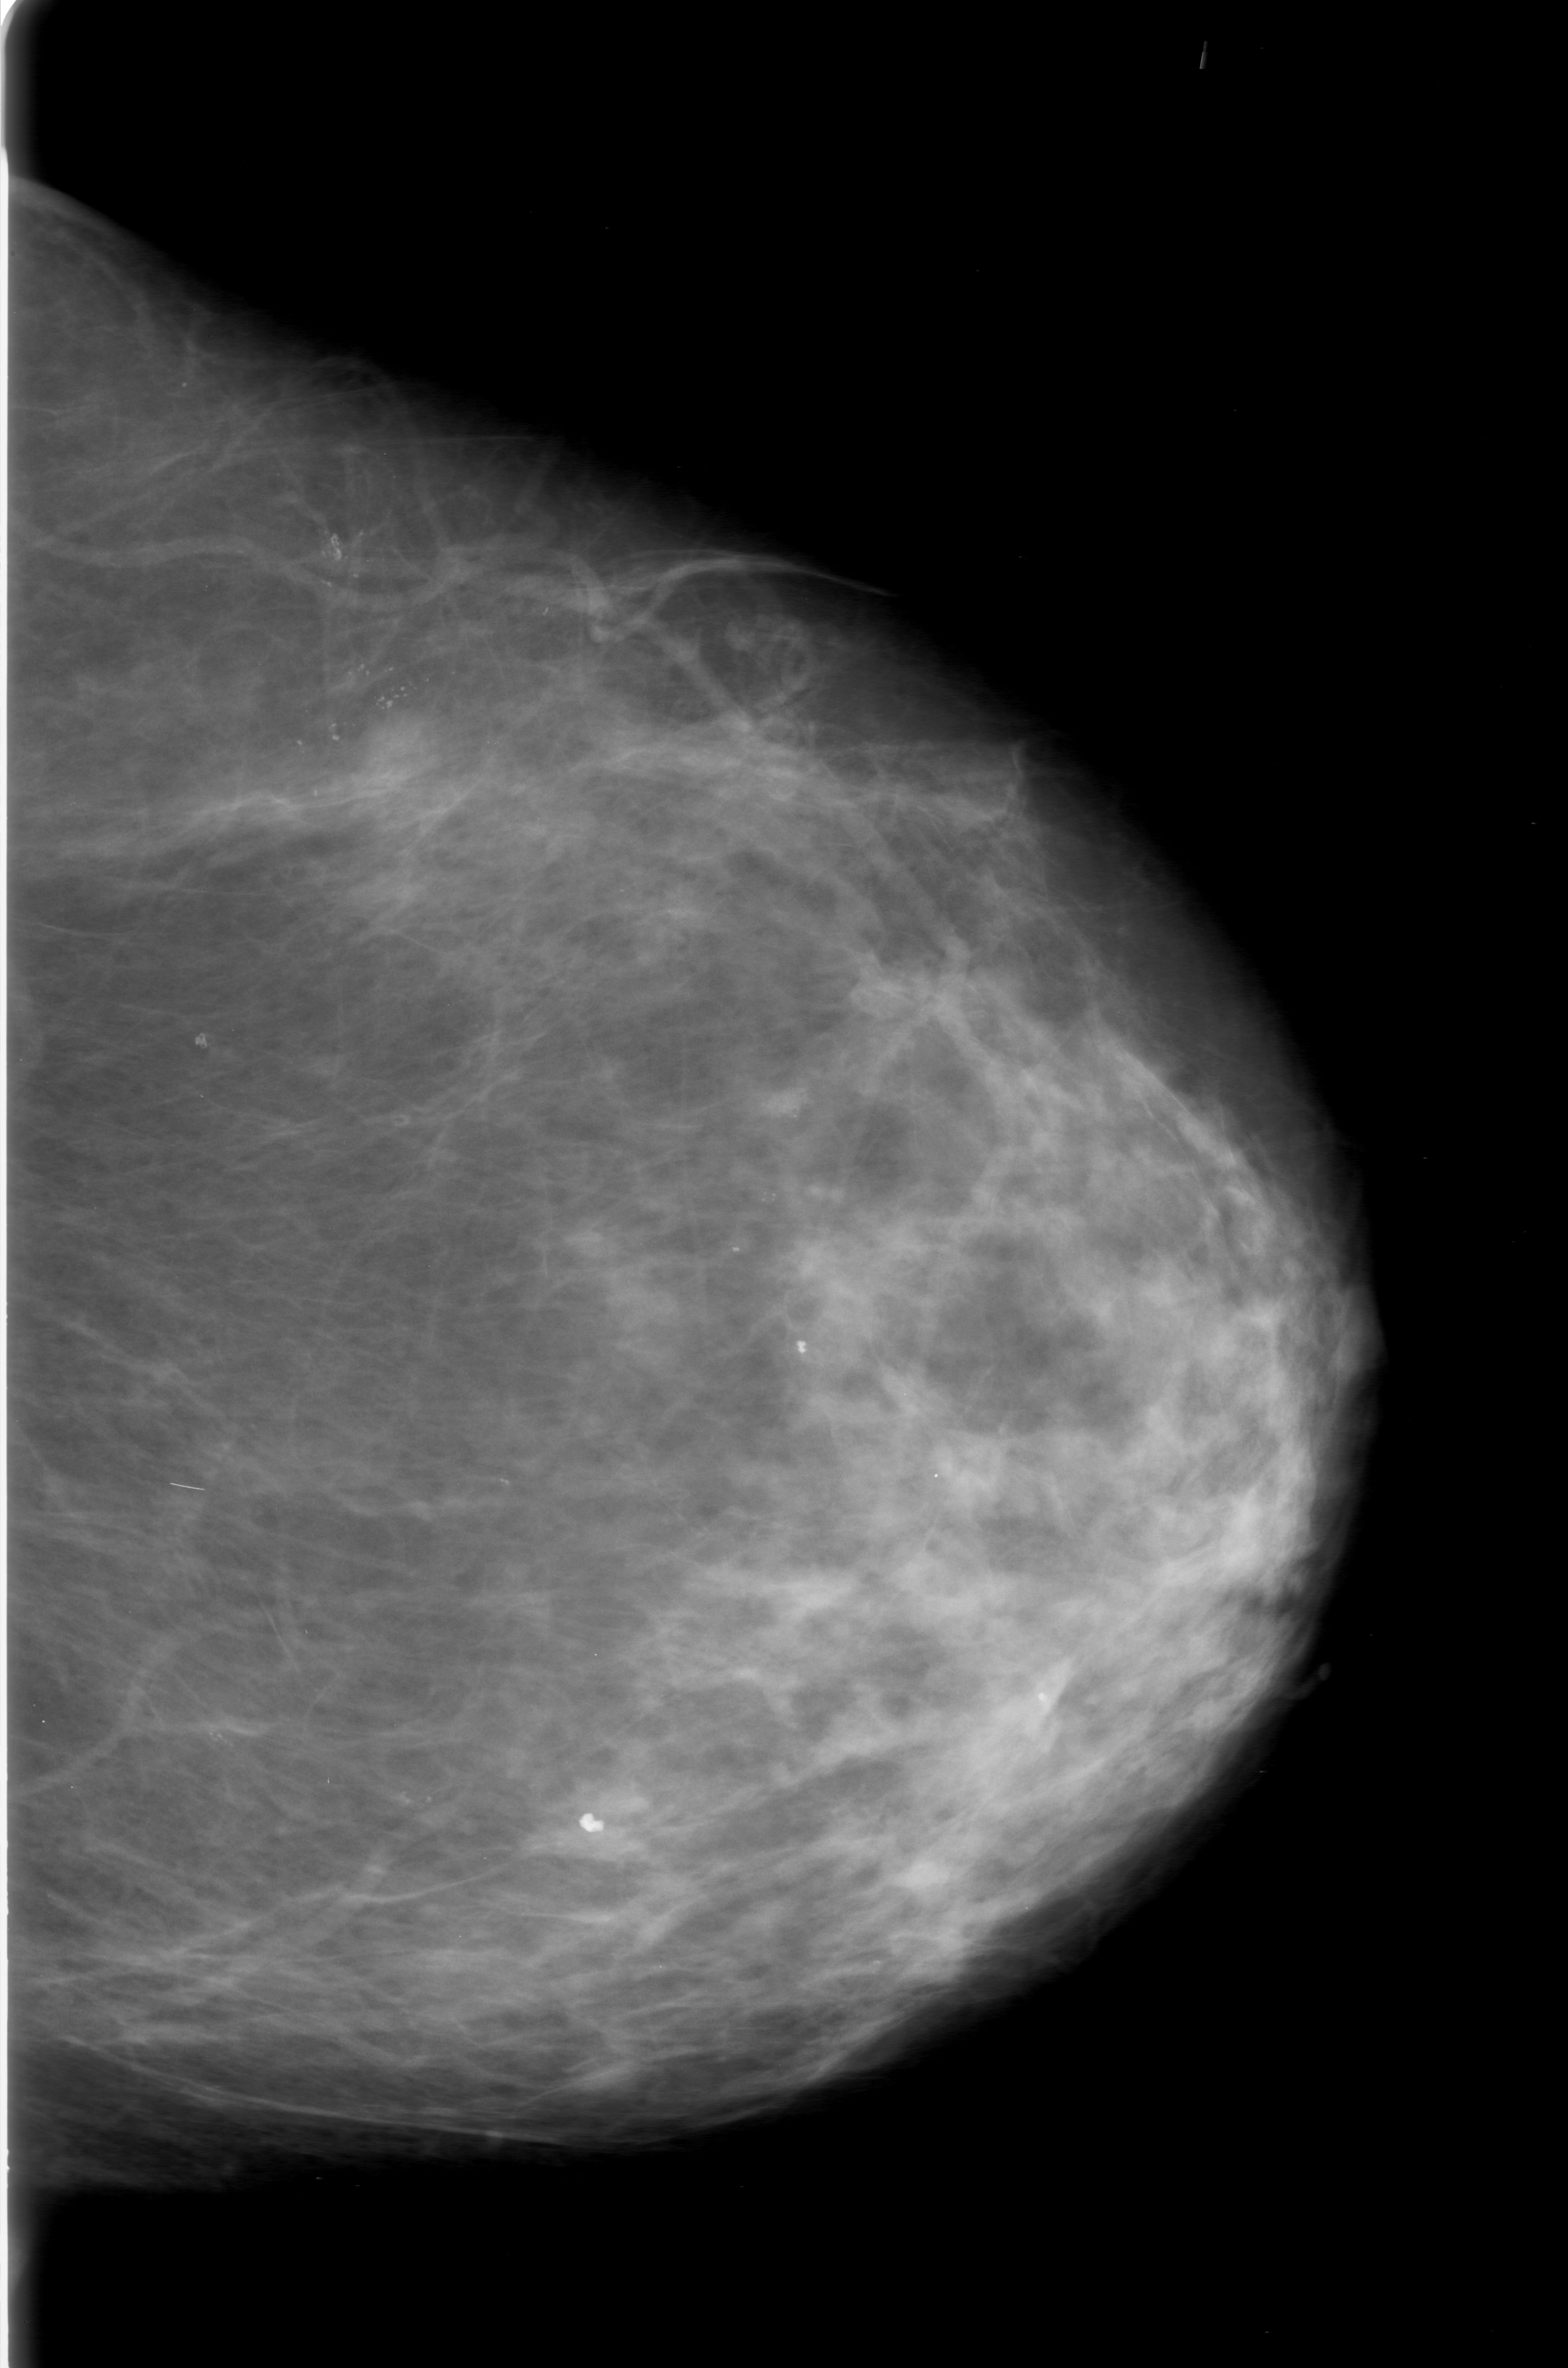
Scanned film-screen mammogram. Left breast. CC view. Breast composition: scattered fibroglandular densities (BI-RADS density category 2 of 4). 1568 × 2368 image matrix.
Marked abnormalities (boxes around the expert regions of interest):
- calcifications, morphology round and regular / pleomorphic, distribution clustered; BI-RADS assessment category 0 (incomplete: needs additional imaging); pathology (as recorded): benign: bounding box [x1, y1, x2, y2] px = [143, 448, 545, 883]